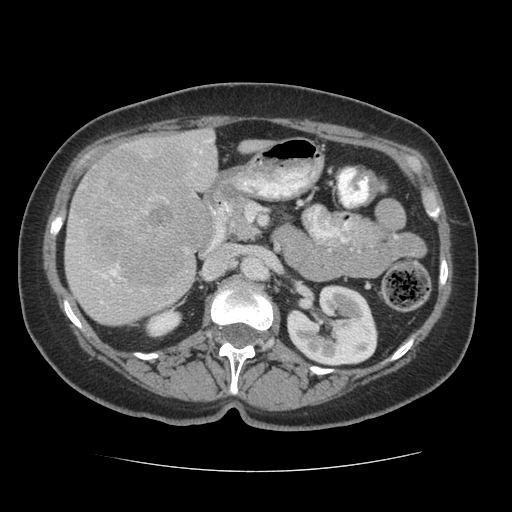
Contrast-enhanced abdominal CT (liver protocol), one axial slice; slice 26 of 75 in the series (ordered by position); reconstruction kernel STANDARD; soft-tissue window (W 400 / L 40 HU); 512 × 512 image matrix, field of view 360 × 360 mm. From the clinical record (not read from this slice): diagnosis: hepatocellular carcinoma (patient treated with transarterial chemoembolisation; whether this scan precedes or follows treatment is not stated here); TNM stage (as recorded): Stage-I; Child-Pugh class: A; tumour differentiation: moderately differentiated; tumour nodularity: uninodular.
Annotated regions visible in this slice (semi-automatic segmentation, software-assisted and operator-edited):
- liver parenchyma outside the tumour (the mass and vessels are separate outlines, so this box may not span the whole liver): bounding box [x1, y1, x2, y2] px = [64, 128, 270, 324]
- mass: [69, 147, 210, 294]
- liver vessels: [68, 139, 212, 304]